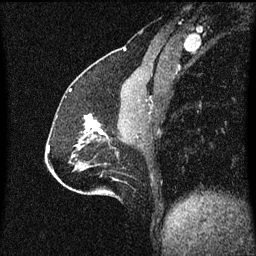
Breast MRI (dynamic contrast-enhanced), one sagittal slice. Position 26 of 60 along the scan axis. Dynamic contrast-enhanced series, image 2 of 3 at this slice position (ordered by acquisition). 1.5 T. TE 4.2 ms, TR 8.4 ms. 2 mm slice thickness. 256 × 256 image matrix, field of view 200 × 200 mm. Female patient, age 51 years.
Outlined on this slice (semi-automatically segmented with operator editing):
- analysis volume of interest (the breast-tissue region the enhancement analysis was run in; not a lesion): bounding box <80,114,109,139> (left, top, right, bottom; pixels)
- tumour enhancement mask (voxels above the 70 % enhancement threshold inside the analysis volume of interest): <84,114,103,135>